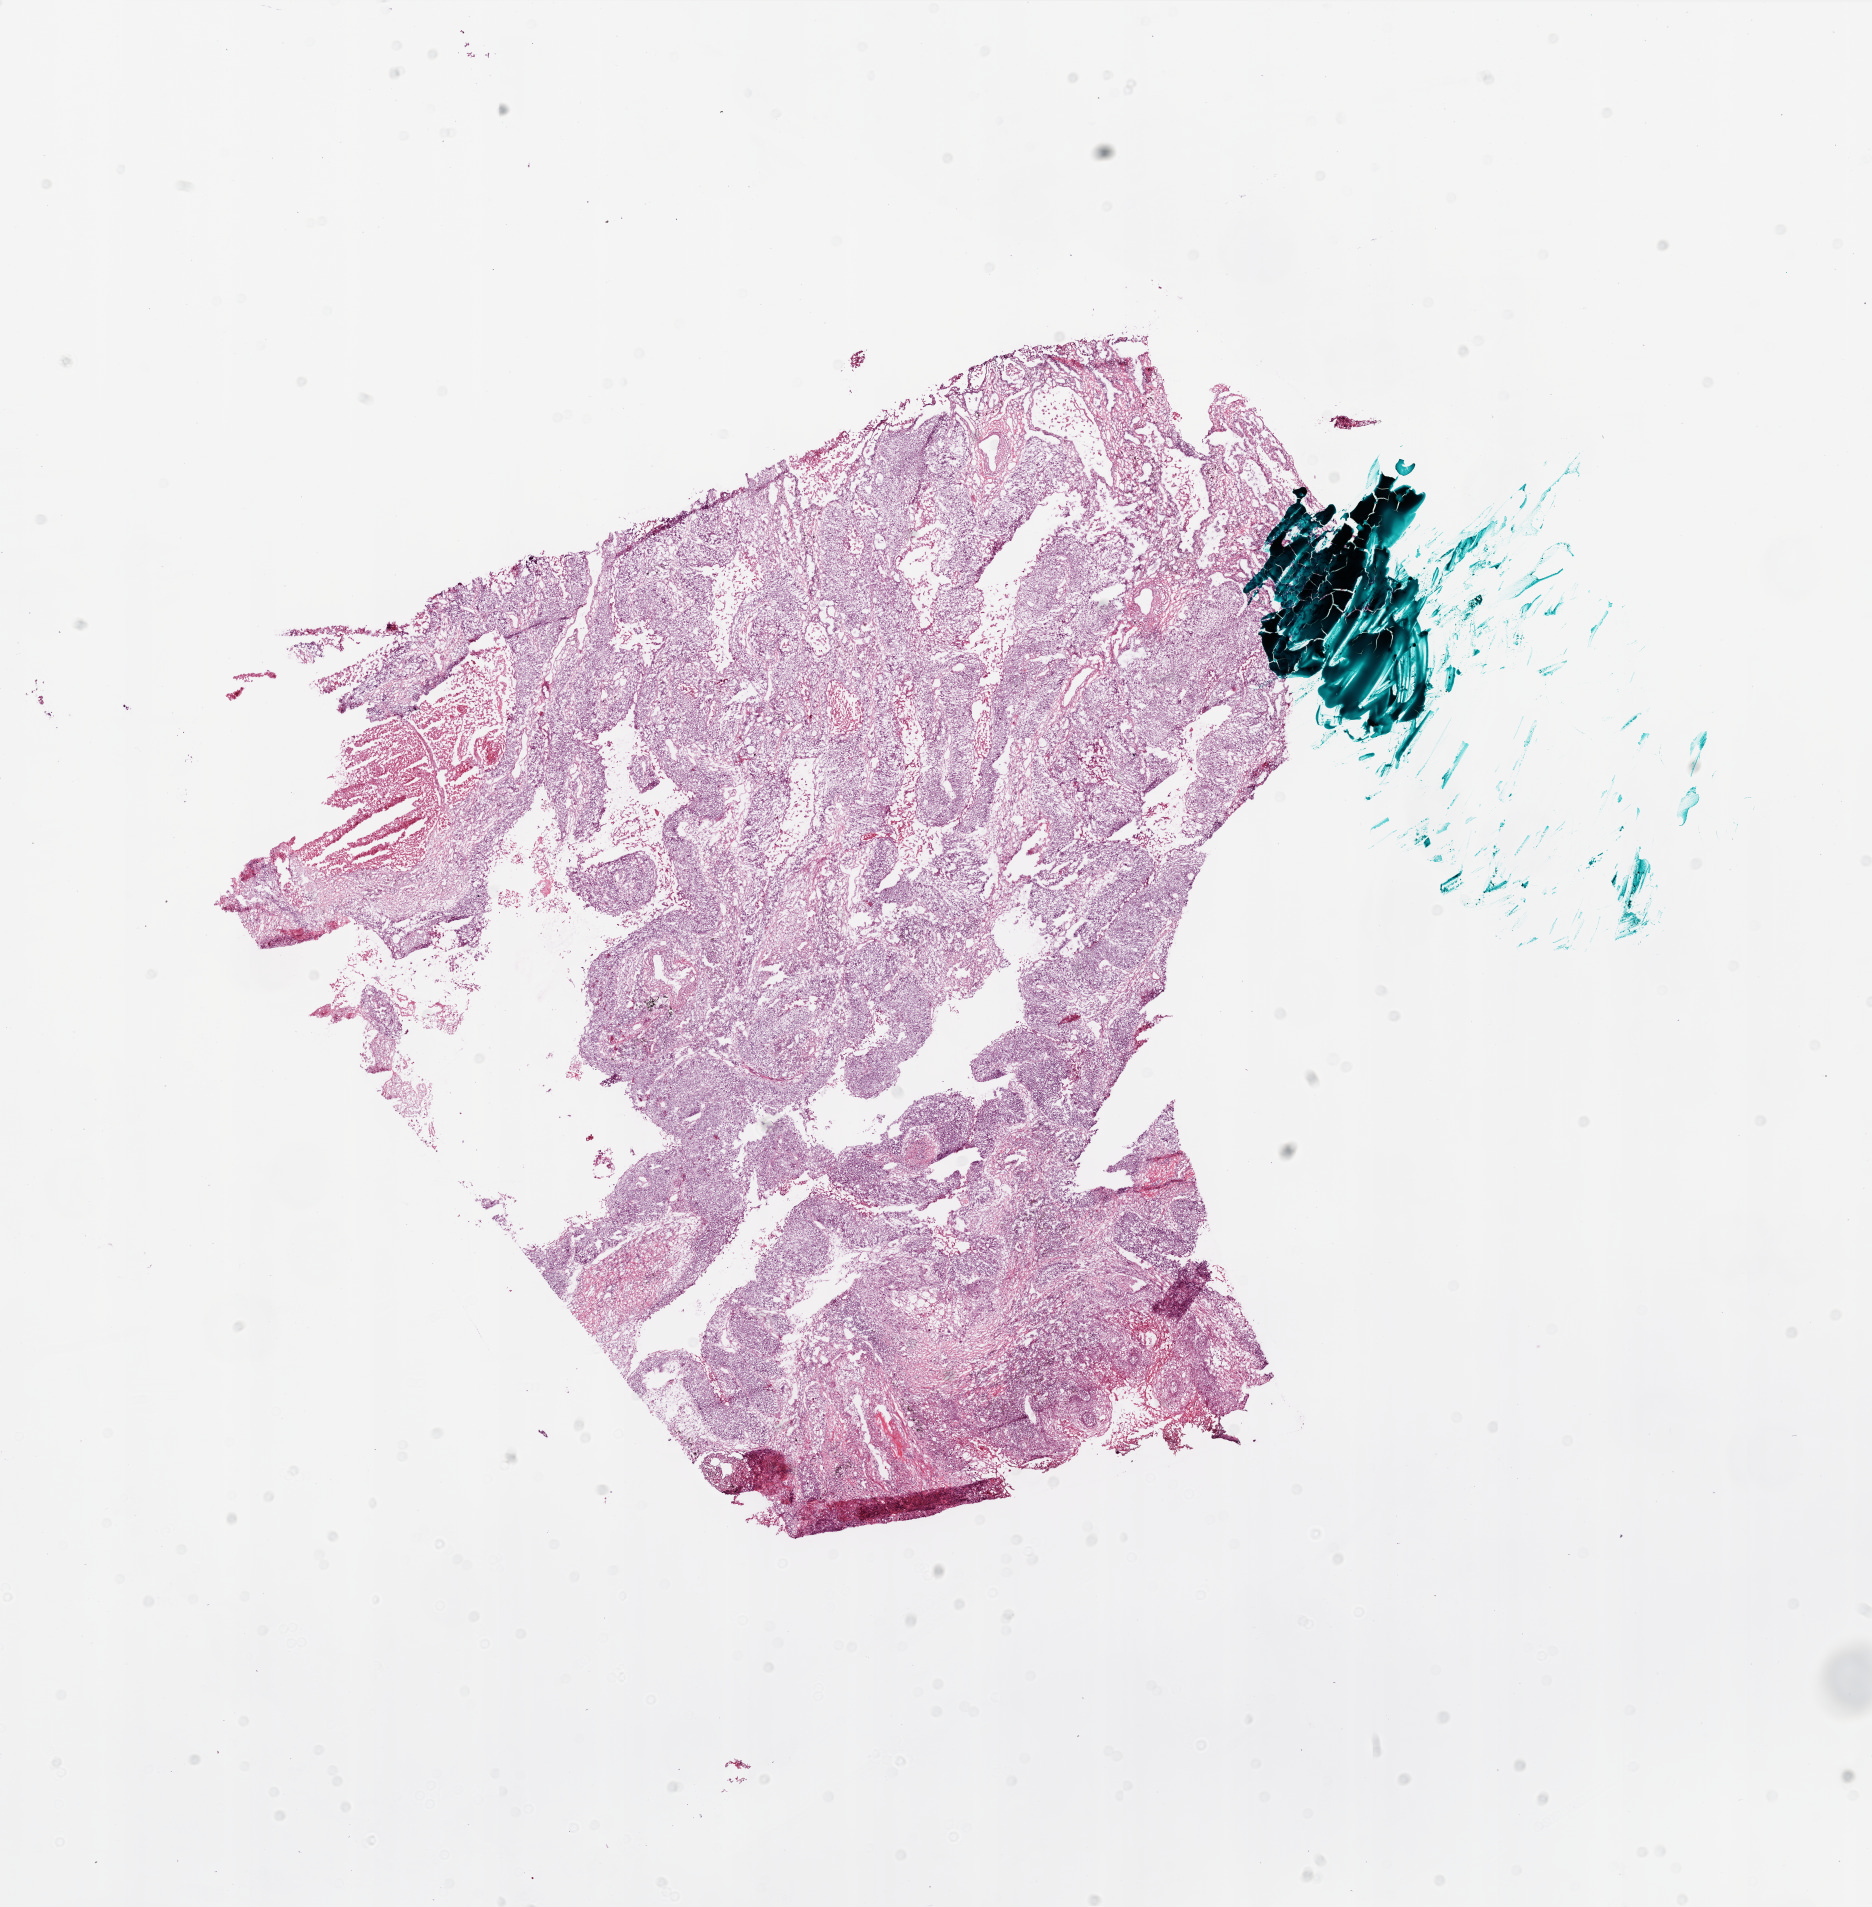
Whole-slide histology image, H&E, low-resolution overview of the scanned area, about 15.0 x 15.3 mm (slide scanned at 20x); frozen section; lung, primary tumour sample. Male patient; age at initial diagnosis 61 years. Slide review estimates, as recorded: tumour nuclei 70%, necrosis 5%.
Pathologic diagnosis: Squamous cell carcinoma, NOS. TNM: T2 N0 M0. AJCC pathologic stage: IB. Laterality: left.